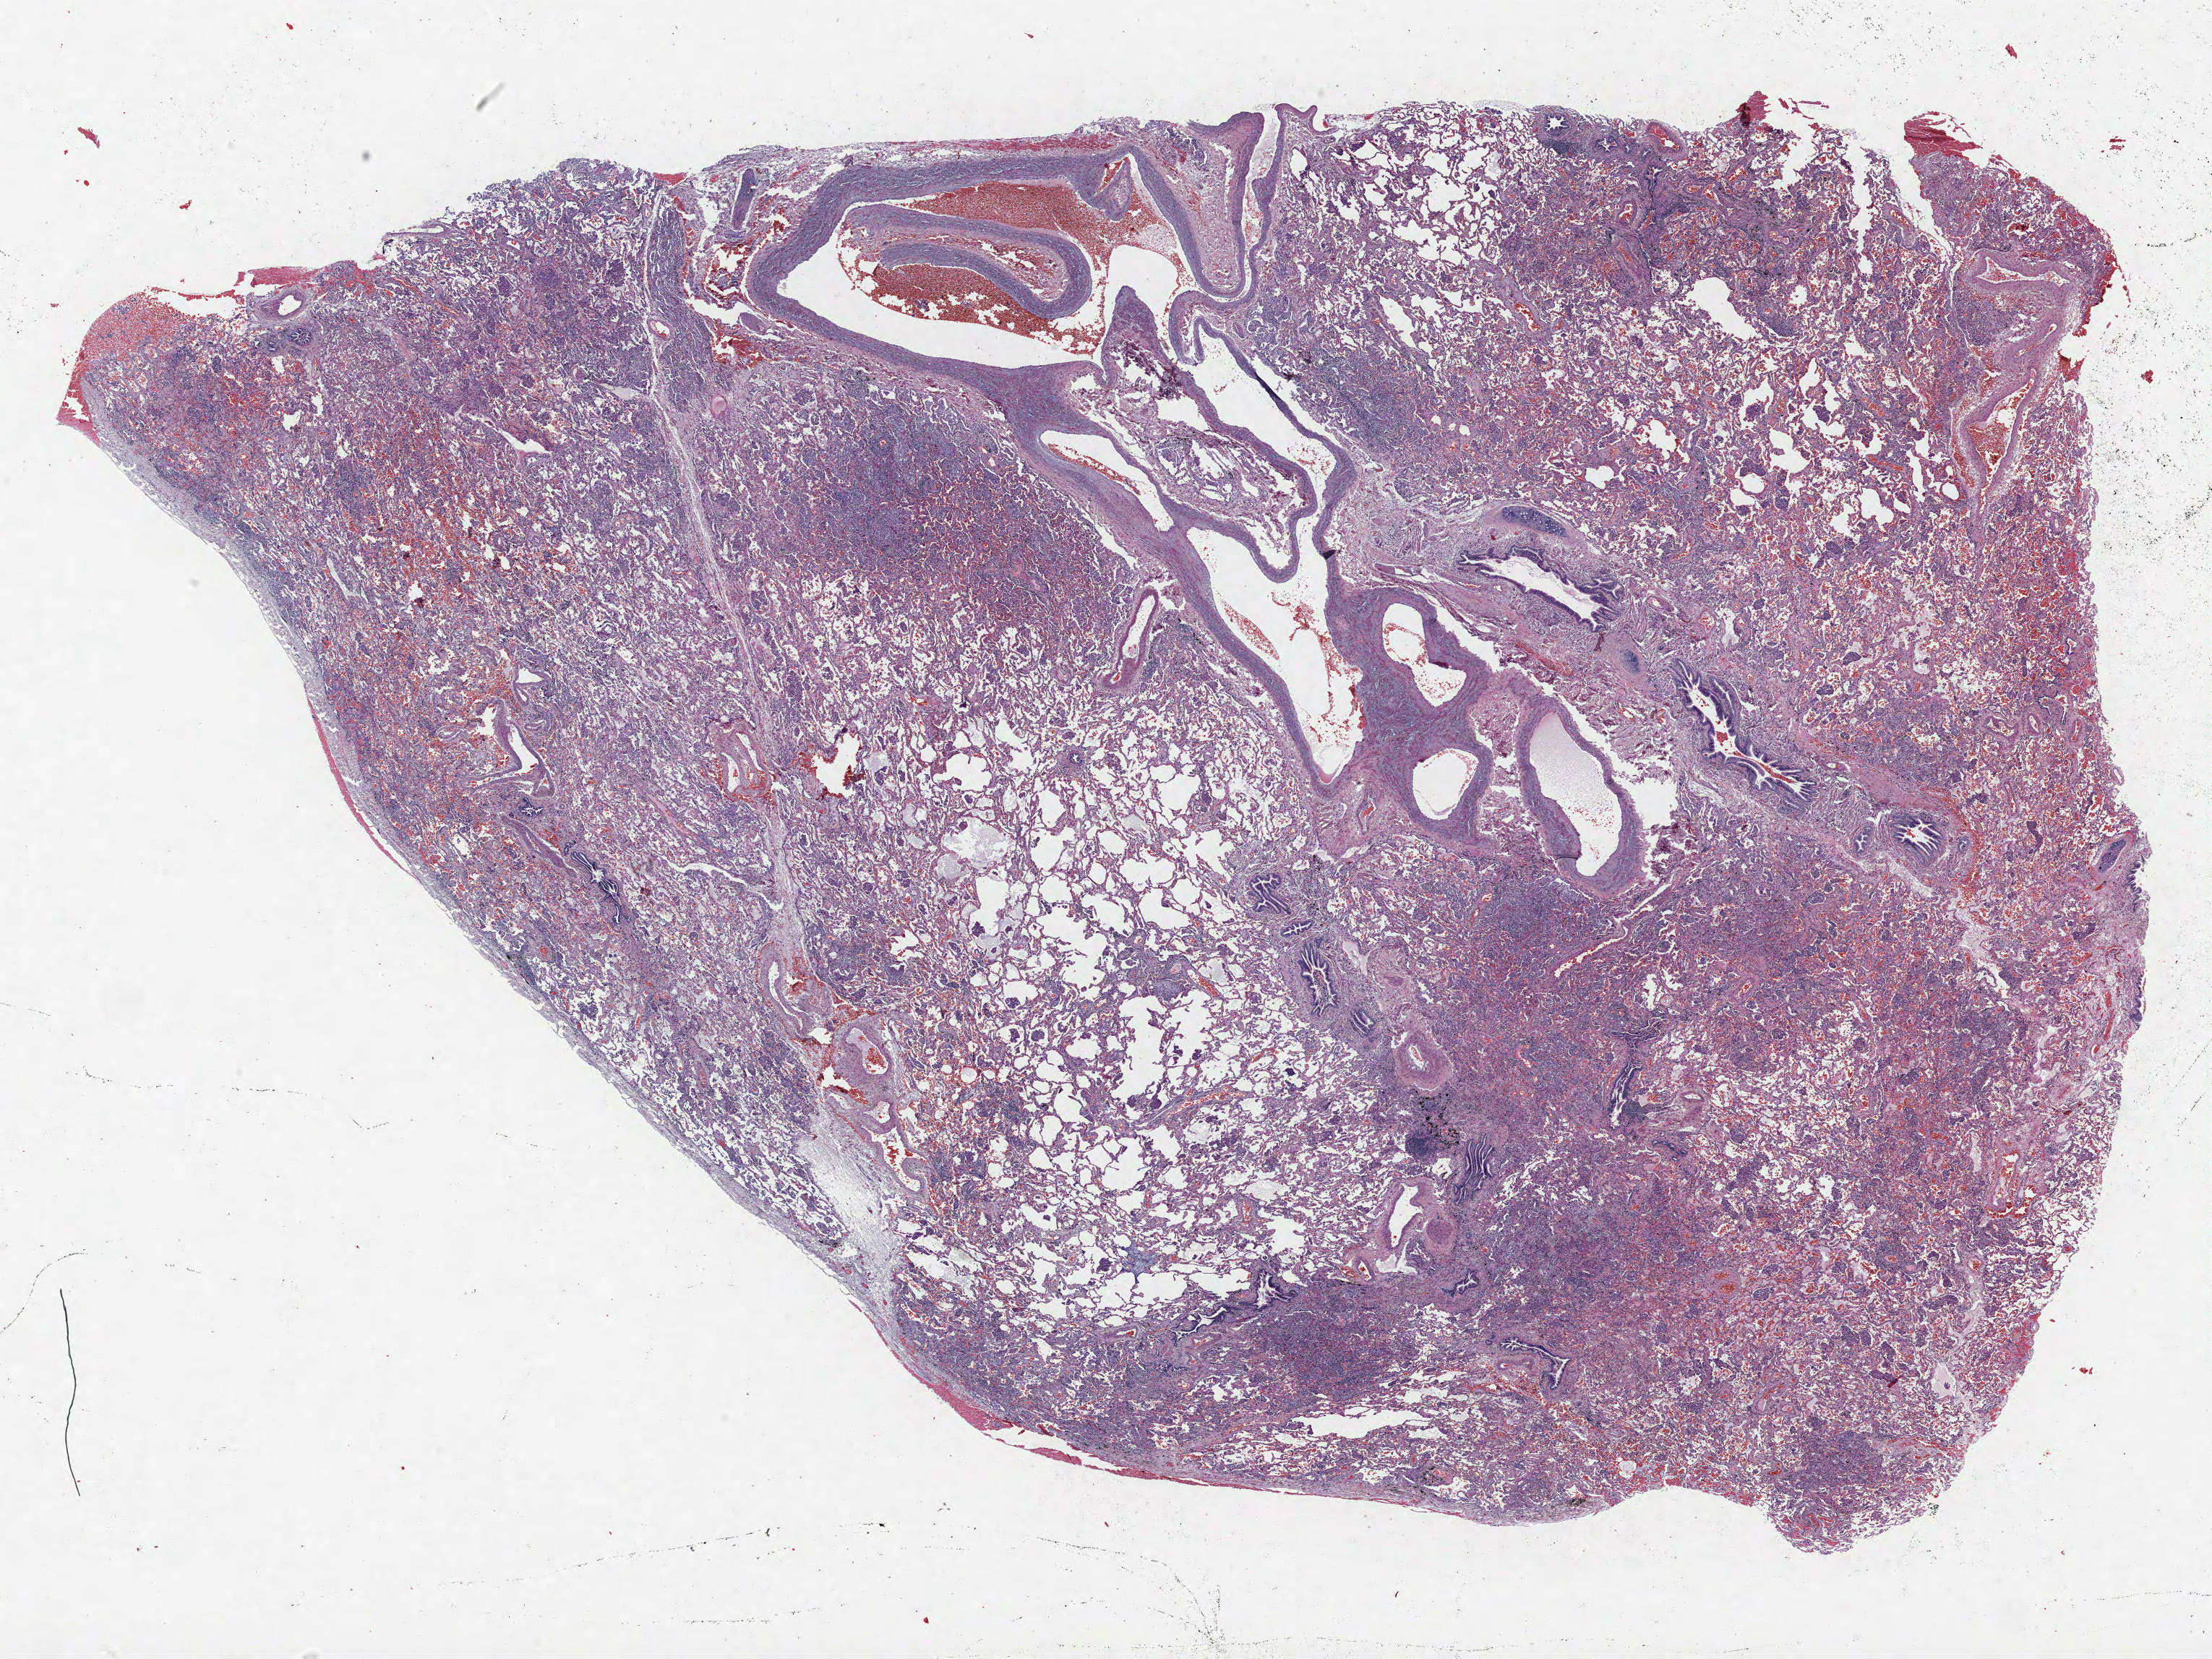
Whole-slide histology image, Hematoxylin and eosin (H&E) stained — whole scanned area (about 24.5 x 18.4 mm, slide scanned at 40x) shown as a low-resolution overview; FFPE section; lung tissue. Male, age 65 at enrolment. Former smoker at enrolment. Grade: poorly differentiated (G3).
Participant's lung-cancer diagnosis: Adenocarcinoma, NOS. Tumour size (pathology): 17 mm. Stage (AJCC 6th edition): IA. Primary tumour location (clinical record): right upper lobe.